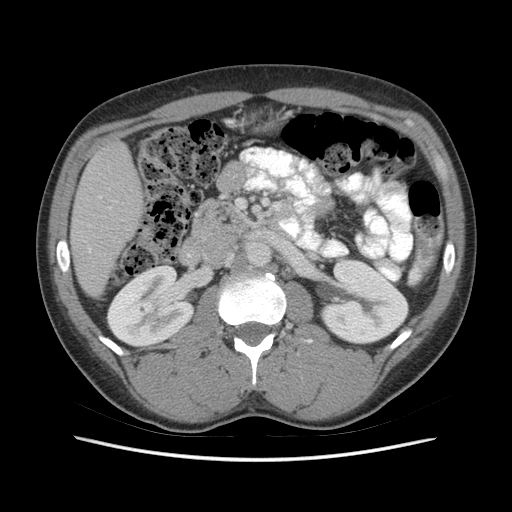
Contrast-enhanced abdominal CT (liver protocol), one axial slice; position 19 of 73 along the scan axis; 140 kVp; soft-tissue window (W 400 / L 40 HU); 2.5 mm slice thickness; 512 × 512 image matrix, field of view 360 × 360 mm. From the clinical record (not read from this slice): diagnosis: hepatocellular carcinoma (patient treated with transarterial chemoembolisation; whether this scan precedes or follows treatment is not stated here); TNM stage (as recorded): Stage-IIIA; Child-Pugh class: A; tumour nodularity: multinodular.
Annotated regions visible in this slice (semi-automatic segmentation, software-assisted and operator-edited):
- liver parenchyma outside the tumour (the mass and vessels are separate outlines, so this box may not span the whole liver): bounding box [x1, y1, x2, y2] px = [70, 140, 144, 296]
- liver vessels: [89, 249, 91, 252]